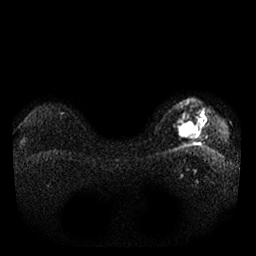
Breast MRI, one axial slice. Position 21 of 25 along the scan axis. Diffusion-weighted series; image 2 of 4 stored at this slice position (different b-values; order by instance number). 1.5 T. 4 mm slice thickness. 256 × 256 image matrix. Female patient.
Annotated regions visible in this slice (expert manual segmentation):
- tumour on diffusion-weighted imaging: box from (x=178, y=118) to (x=198, y=138) px